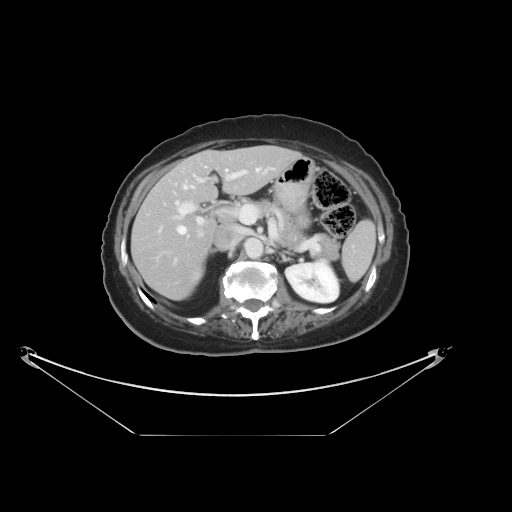
Contrast-enhanced abdominal CT, one axial slice; slice 20 of 36 in the series (ordered by position); reconstruction kernel STANDARD; 120 kVp; intravenous contrast given; soft-tissue window (W 400 / L 40 HU); 5 mm slice thickness; 512 × 512 image matrix, field of view 500 × 500 mm. Female patient, age 70 years. Case-level facts recorded for this patient, not image findings: diagnosis: colorectal cancer liver metastases, imaged before liver resection; multiple liver metastases: no; largest metastasis: 2.5 cm; chemotherapy before resection: no.
Annotated regions visible in this slice (expert manual segmentation):
- hepatic veins: bounding box <156,168,260,239> (left, top, right, bottom; pixels)
- liver: <132,146,298,300>
- planned liver remnant (the part of the liver to remain after resection): <132,146,298,300>
- portal vein (with intrahepatic branches): <174,170,246,263>